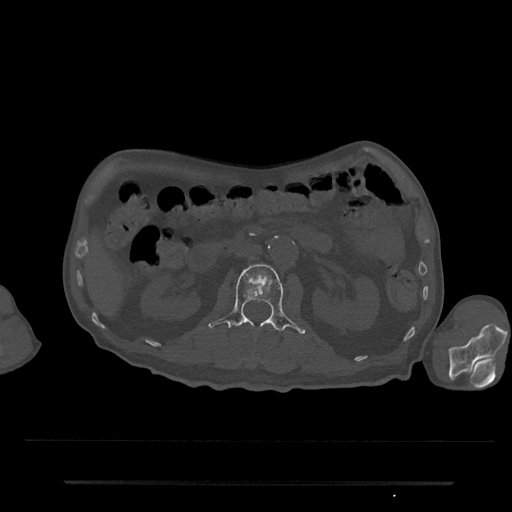
CT including the spine, one axial slice; slice 73 of 797 in the series (ordered by position); reconstruction kernel Br40s/3; 120 kVp; bone window (W 1800 / L 400 HU); 0.5 mm slice thickness; 512 × 512 image matrix, field of view 427 × 427 mm. Patient: male, 74 years. From the clinical record (not read from this slice): primary cancer: prostate.
Annotated regions visible in this slice (semi-automatic segmentation, software-assisted and operator-edited):
- L1 vertebra: box from (x=267, y=325) to (x=272, y=333) px
- L2 vertebra: (x=208, y=264)–(x=305, y=334)